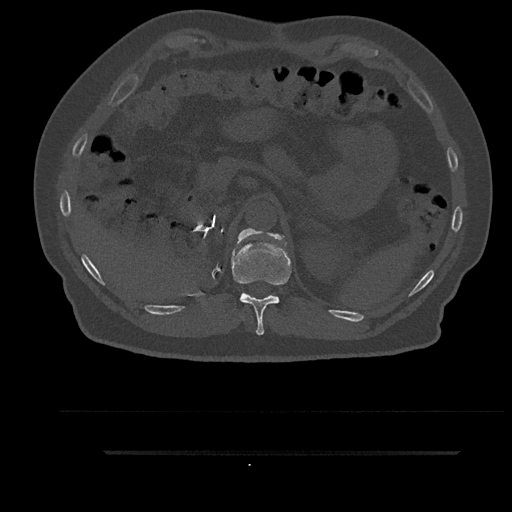
CT including the spine, one axial slice. Slice 289 of 797 in the series (ordered by position). Reconstruction kernel Br40s/3. Bone window (W 1800 / L 400 HU). 0.5 mm slice thickness. 512 × 512 image matrix. Patient: male, 63 years. Case-level facts recorded for this patient, not image findings: primary cancer: renal; vertebrae with lytic lesions (as recorded): T8.
Outlined on this slice (semi-automatically segmented with operator editing):
- T11 vertebra: bounding box (x1, y1, x2, y2) in pixels: (231, 229, 291, 335)
- T12 vertebra: (238, 228, 261, 241)